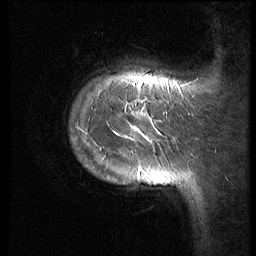
Breast MRI (dynamic contrast-enhanced), one sagittal slice. Position 11 of 70 along the scan axis. 3 images stored at this slice position (order not interpretable as contrast timing). 1.5 T. TE 4.2 ms, TR 9 ms. 2.5 mm slice thickness. 256 × 256 image matrix, field of view 180 × 180 mm. Patient: female, 28 years. From the clinical record (not read from this slice): setting: breast cancer imaged before/during neoadjuvant chemotherapy.
Structures marked on this image (semi-automatic segmentation, software-assisted and operator-edited):
- analysis volume of interest (the breast-tissue region the enhancement analysis was run in; not a lesion): bounding box (x1, y1, x2, y2) in pixels: (67, 45, 186, 213)
- tumour enhancement mask (voxels above the 140 % enhancement threshold inside the analysis volume of interest): (115, 81, 171, 186)